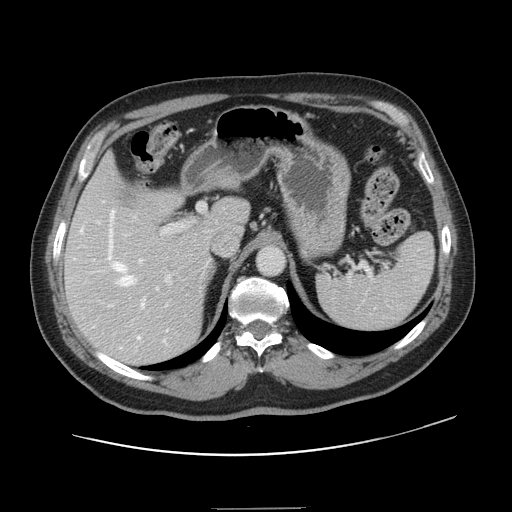
Contrast-enhanced abdominal CT, one axial slice. Slice 95 of 143 in the series (ordered by position). Intravenous contrast given. Soft-tissue window (W 400 / L 40 HU). 512 × 512 image matrix, field of view 402 × 402 mm. Male patient, age 62 years. From the clinical record (not read from this slice): diagnosis: colorectal cancer liver metastases, imaged before liver resection; multiple liver metastases: yes; largest metastasis: 2.7 cm; chemotherapy before resection: yes.
Annotated regions visible in this slice (outlined manually by an expert reader):
- hepatic veins: bounding box [x1, y1, x2, y2] px = [80, 201, 166, 349]
- liver: [66, 158, 248, 364]
- planned liver remnant (the part of the liver to remain after resection): [68, 158, 248, 254]
- portal vein (with intrahepatic branches): [74, 203, 205, 307]